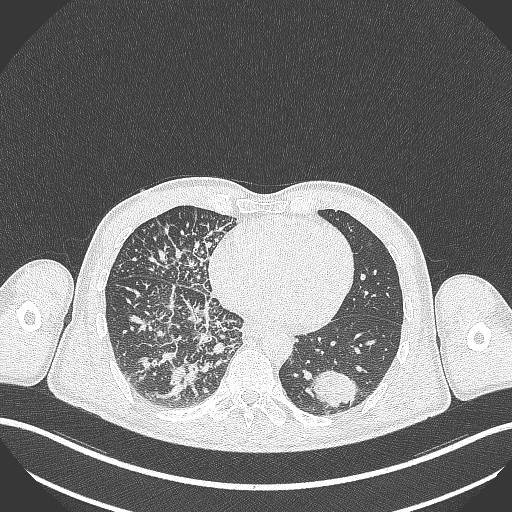
Chest CT, one axial slice; position 108 of 348 along the scan axis; reconstruction kernel B70f; 120 kVp; lung window (W 1500 / L -600 HU); 512 × 512 image matrix, field of view 400 × 400 mm. Patient: male, 49 years. Case-level facts recorded for this patient, not image findings: clinical TNM (as recorded): T2b N1 M0.
Outlined on this slice (rectangle marked by the reading radiologist):
- lung tumour (recorded histology: adenocarcinoma): bounding box <311,368,362,411> (left, top, right, bottom; pixels)